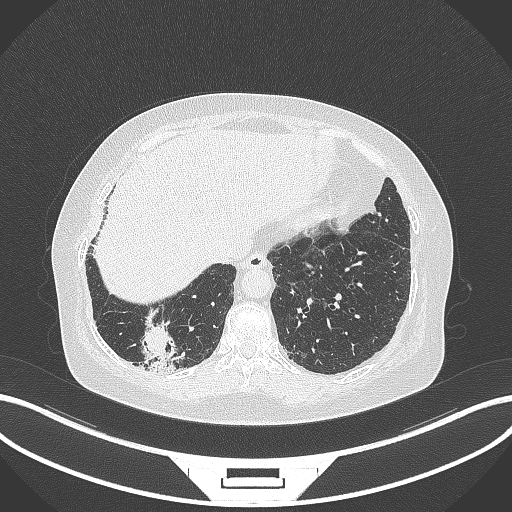
Chest CT, one axial slice. Position 33 of 296 along the scan axis. Lung window (W 1500 / L -600 HU). 1 mm slice thickness. 512 × 512 image matrix. Patient: female, 65 years. Case-level facts recorded for this patient, not image findings: clinical TNM (as recorded): T2b N1 M0; histopathological grade: G1.
Annotated regions visible in this slice (bounding box drawn by a radiologist):
- lung tumour (recorded histology: adenocarcinoma): bounding box (x1, y1, x2, y2) in pixels: (138, 315, 179, 372)